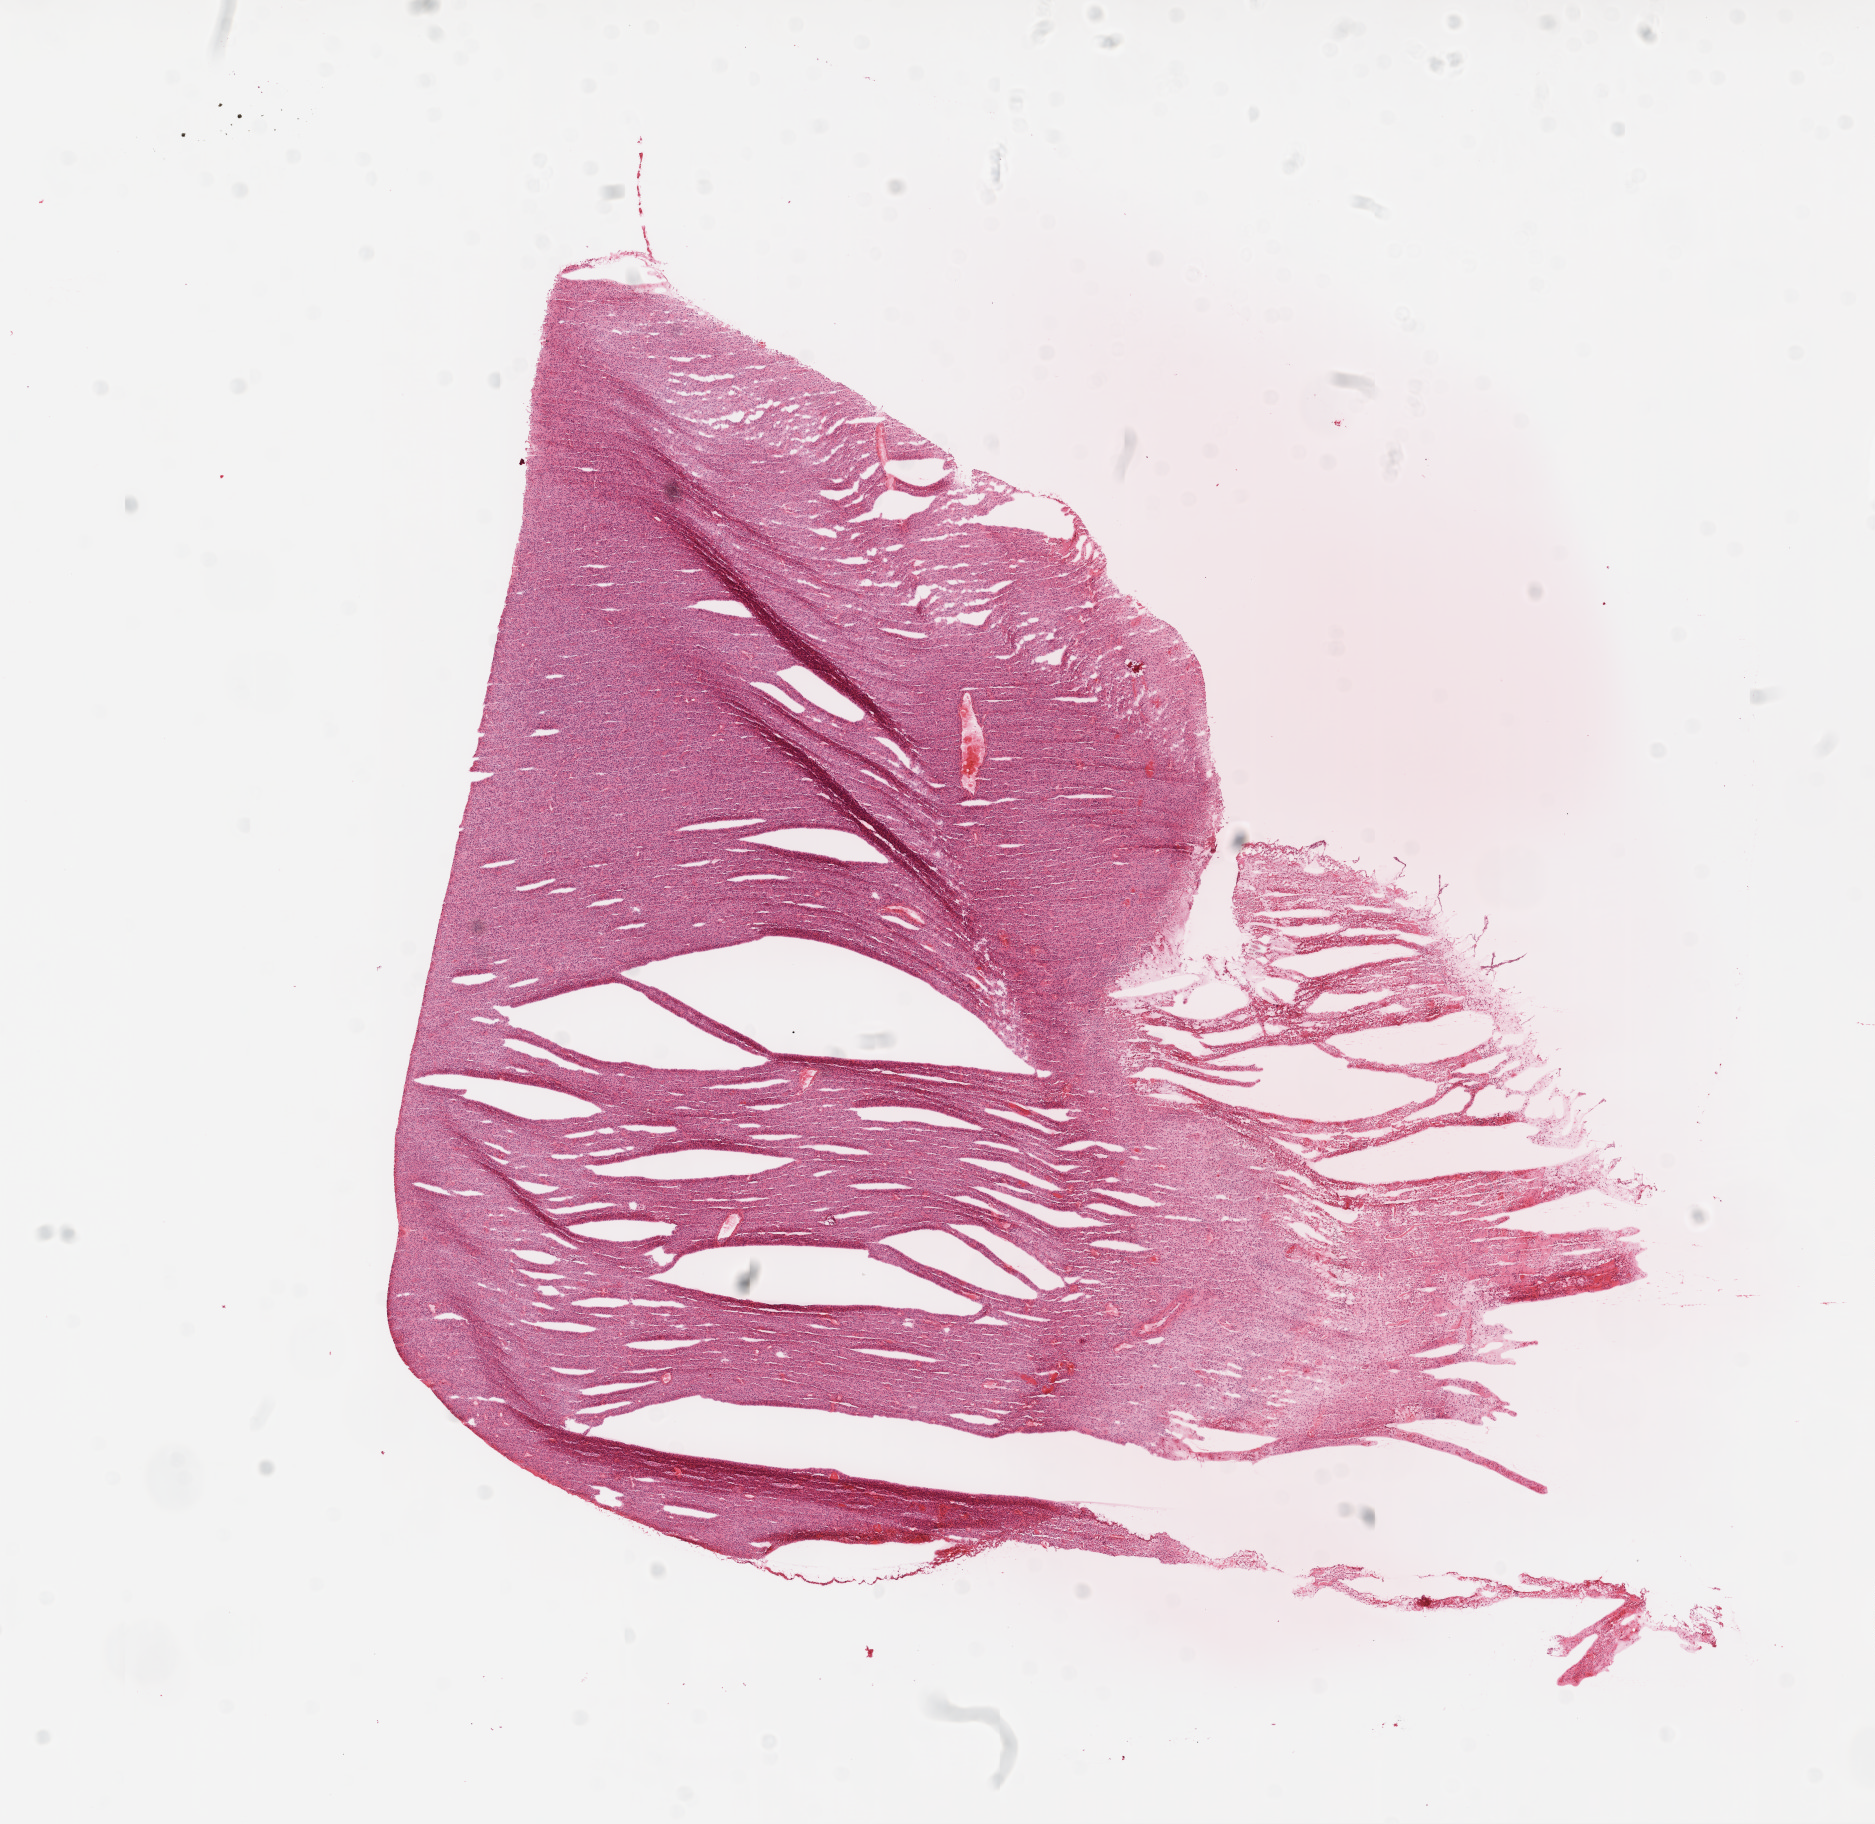
Whole-slide histology image, H&E-stained — whole scanned area (about 15.0 x 14.6 mm) shown as a low-resolution overview; frozen section from the top of the tissue portion; brain, primary tumour sample. Male patient; age at initial diagnosis 60 years. Slide review estimates, as recorded: tumour cells 88%, tumour nuclei 85%, normal cells 0%, stromal cells 0%, necrosis 12%.
Pathologic diagnosis: Glioblastoma.